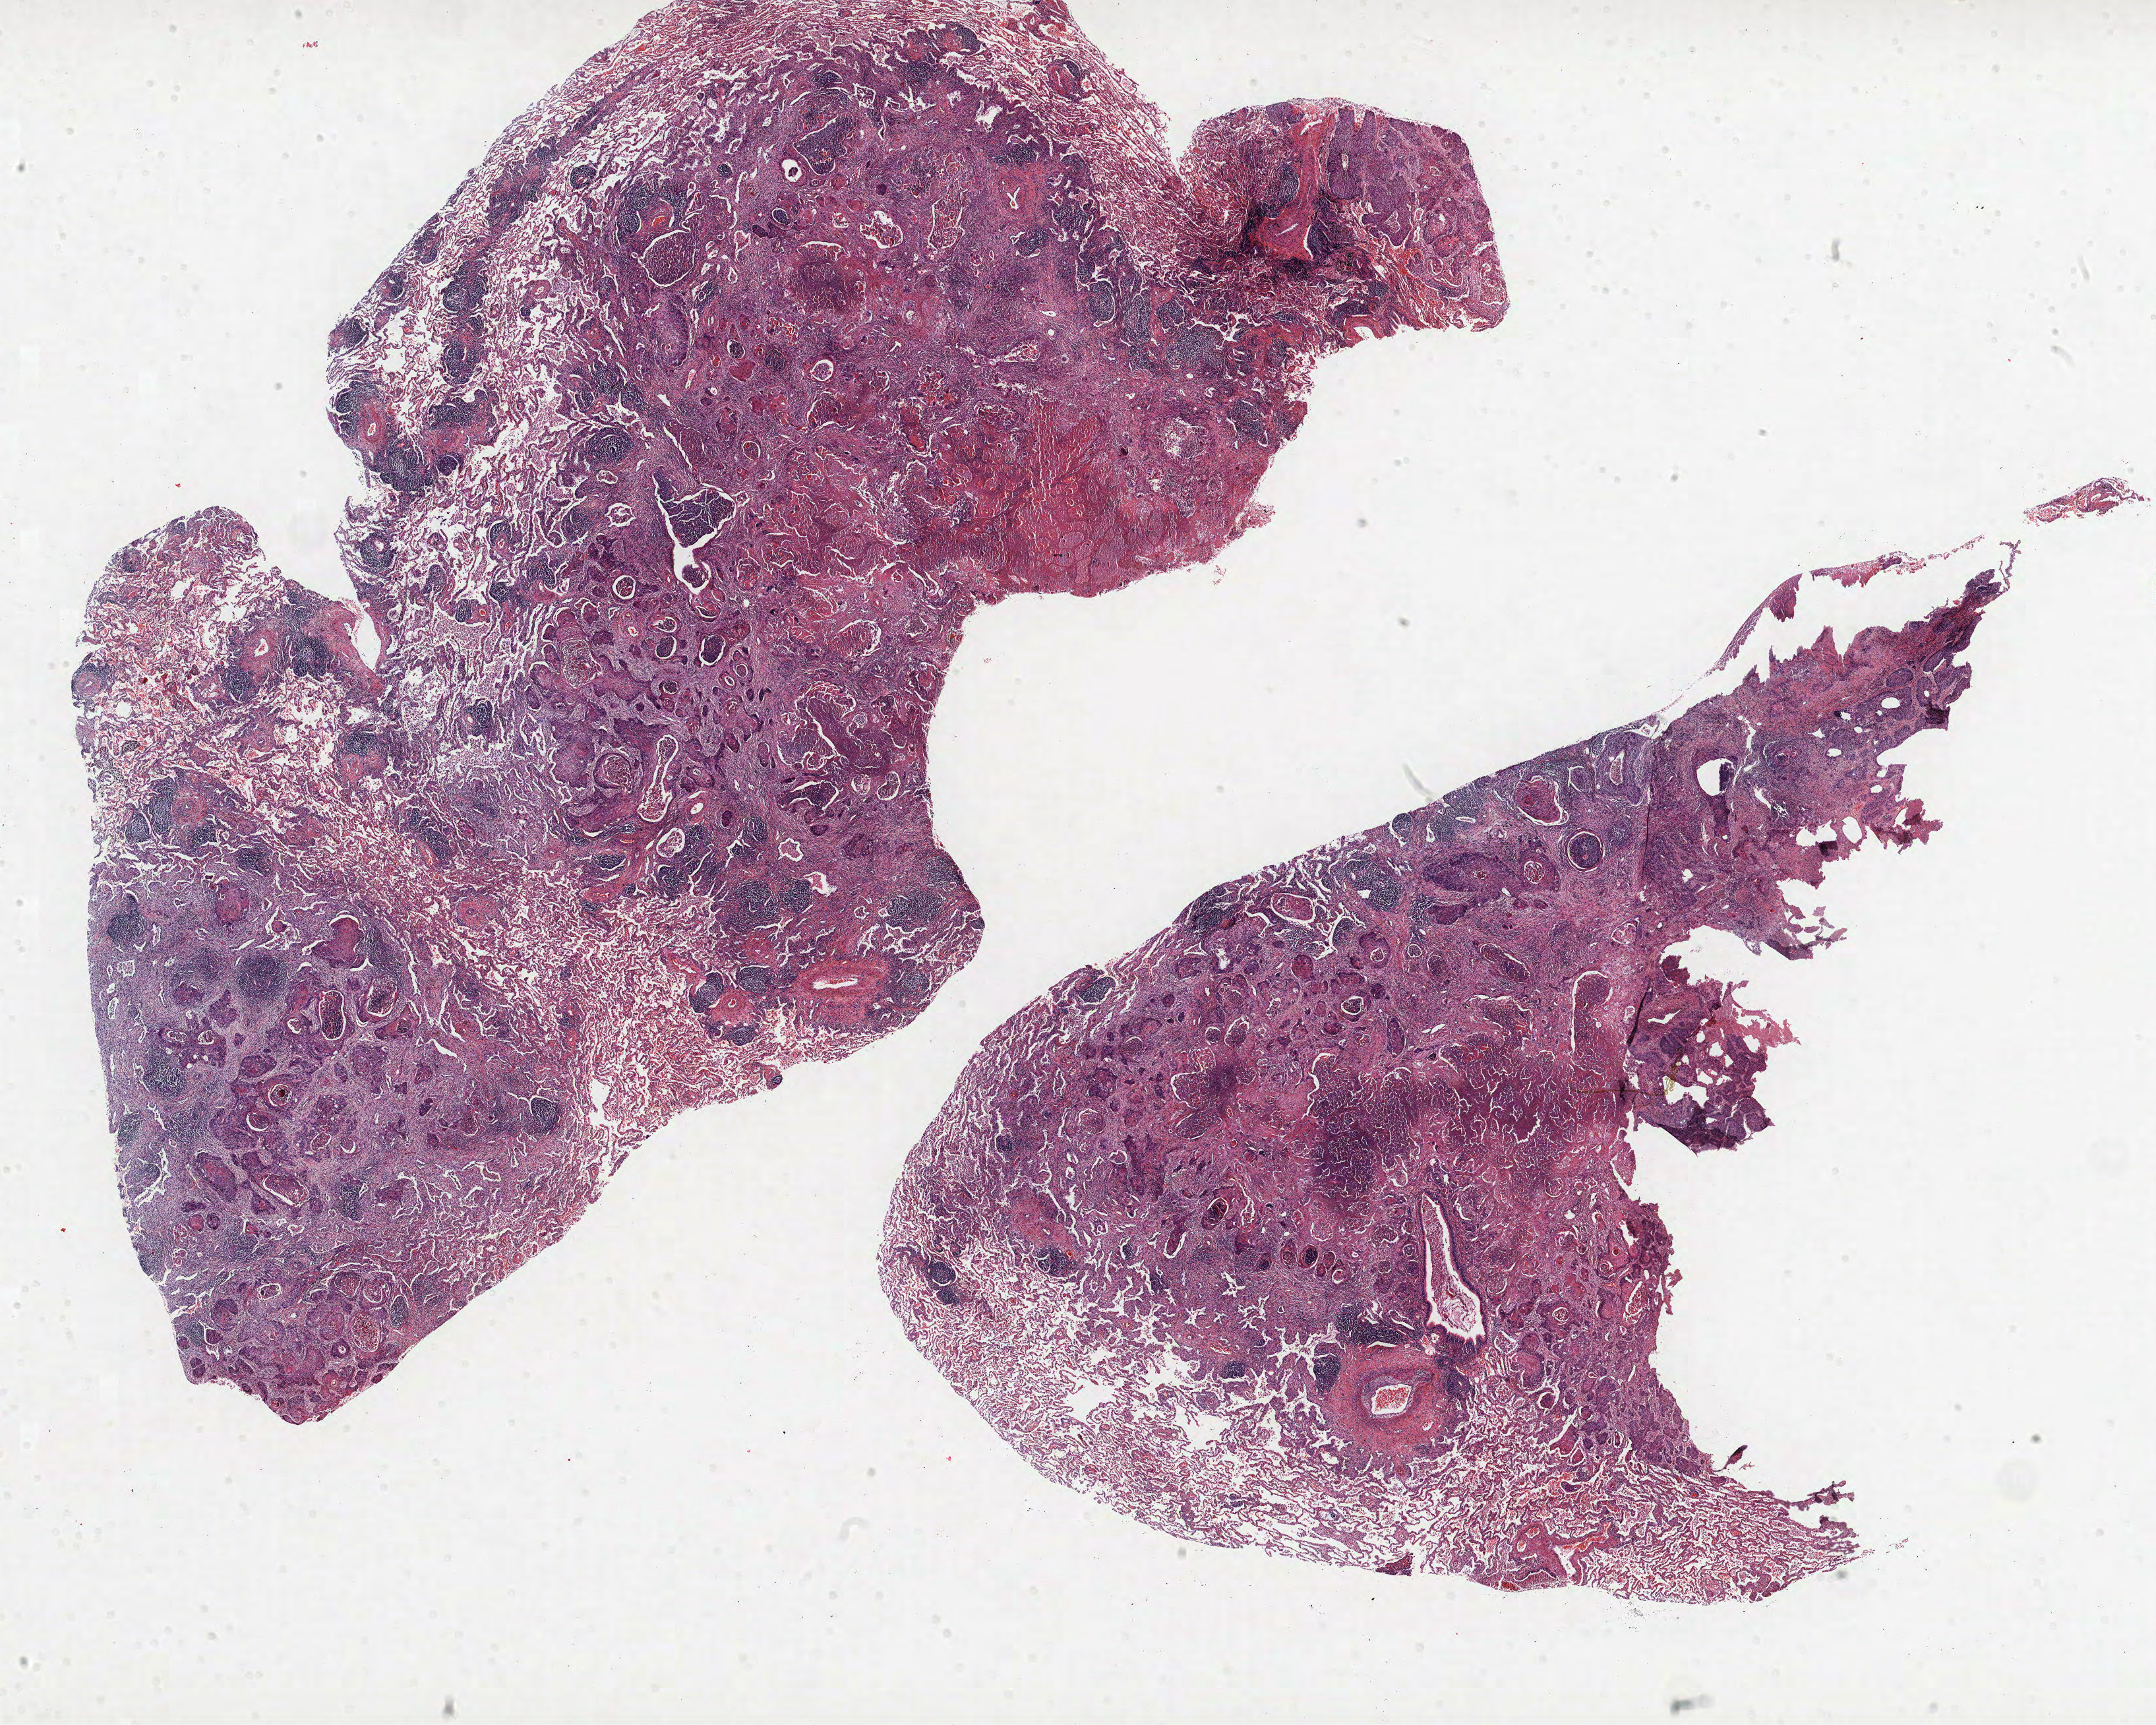
H&E-stained whole-slide image — whole scanned area (about 26.2 x 20.9 mm, from a 40x scan) shown as a low-resolution overview. FFPE section. Lung tissue. Female patient, aged 58 at enrolment. Former smoker at enrolment. Grade: moderately differentiated (G2).
• stage (AJCC 6th edition): IA
• tumour size (pathology): 22 mm
• primary tumour location (clinical record): left upper lobe
• participant's lung-cancer diagnosis: Squamous cell carcinoma, NOS